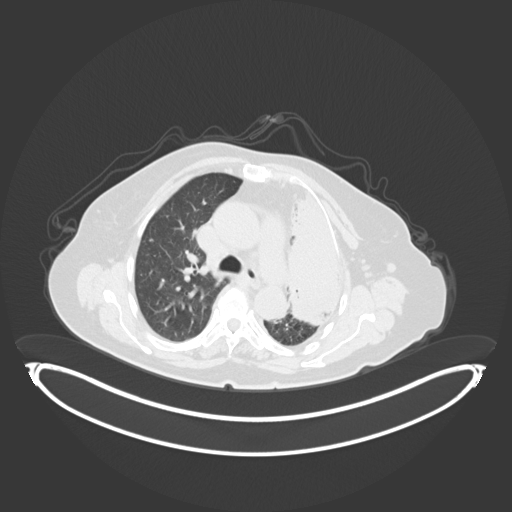
Chest CT, one axial slice. Slice 212 of 284 in the series (ordered by position). Reconstruction kernel B30f. Lung window (W 1500 / L -600 HU). 512 × 512 image matrix. Patient: female, 75 years. From the clinical record (not read from this slice): clinical TNM (as recorded): T3 N3 M1.
Annotated regions visible in this slice (bounding box drawn by a radiologist):
- lung tumour (recorded histology: adenocarcinoma): box from (x=281, y=191) to (x=350, y=331) px